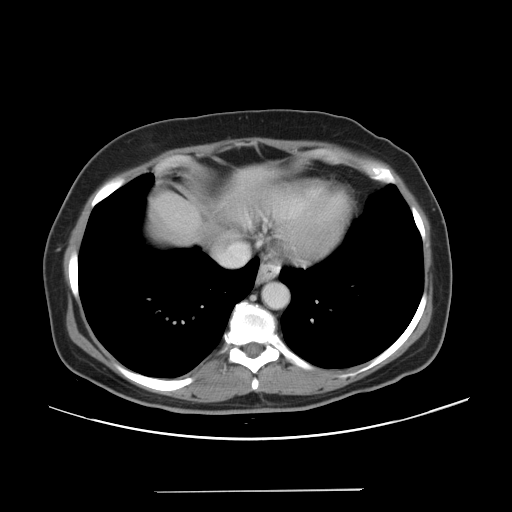
Contrast-enhanced abdominal CT, one axial slice; slice 44 of 56 in the series (ordered by position); intravenous contrast given; soft-tissue window (W 400 / L 40 HU); 5 mm slice thickness; 512 × 512 image matrix. Female patient, age 54 years. Case-level facts recorded for this patient, not image findings: diagnosis: colorectal cancer liver metastases, imaged before liver resection; multiple liver metastases: yes; largest metastasis: 3.2 cm; chemotherapy before resection: yes.
Structures marked on this image (outlined manually by an expert reader):
- liver: box from (x=148, y=169) to (x=270, y=246) px
- planned liver remnant (the part of the liver to remain after resection): (x=224, y=168)–(x=271, y=225)